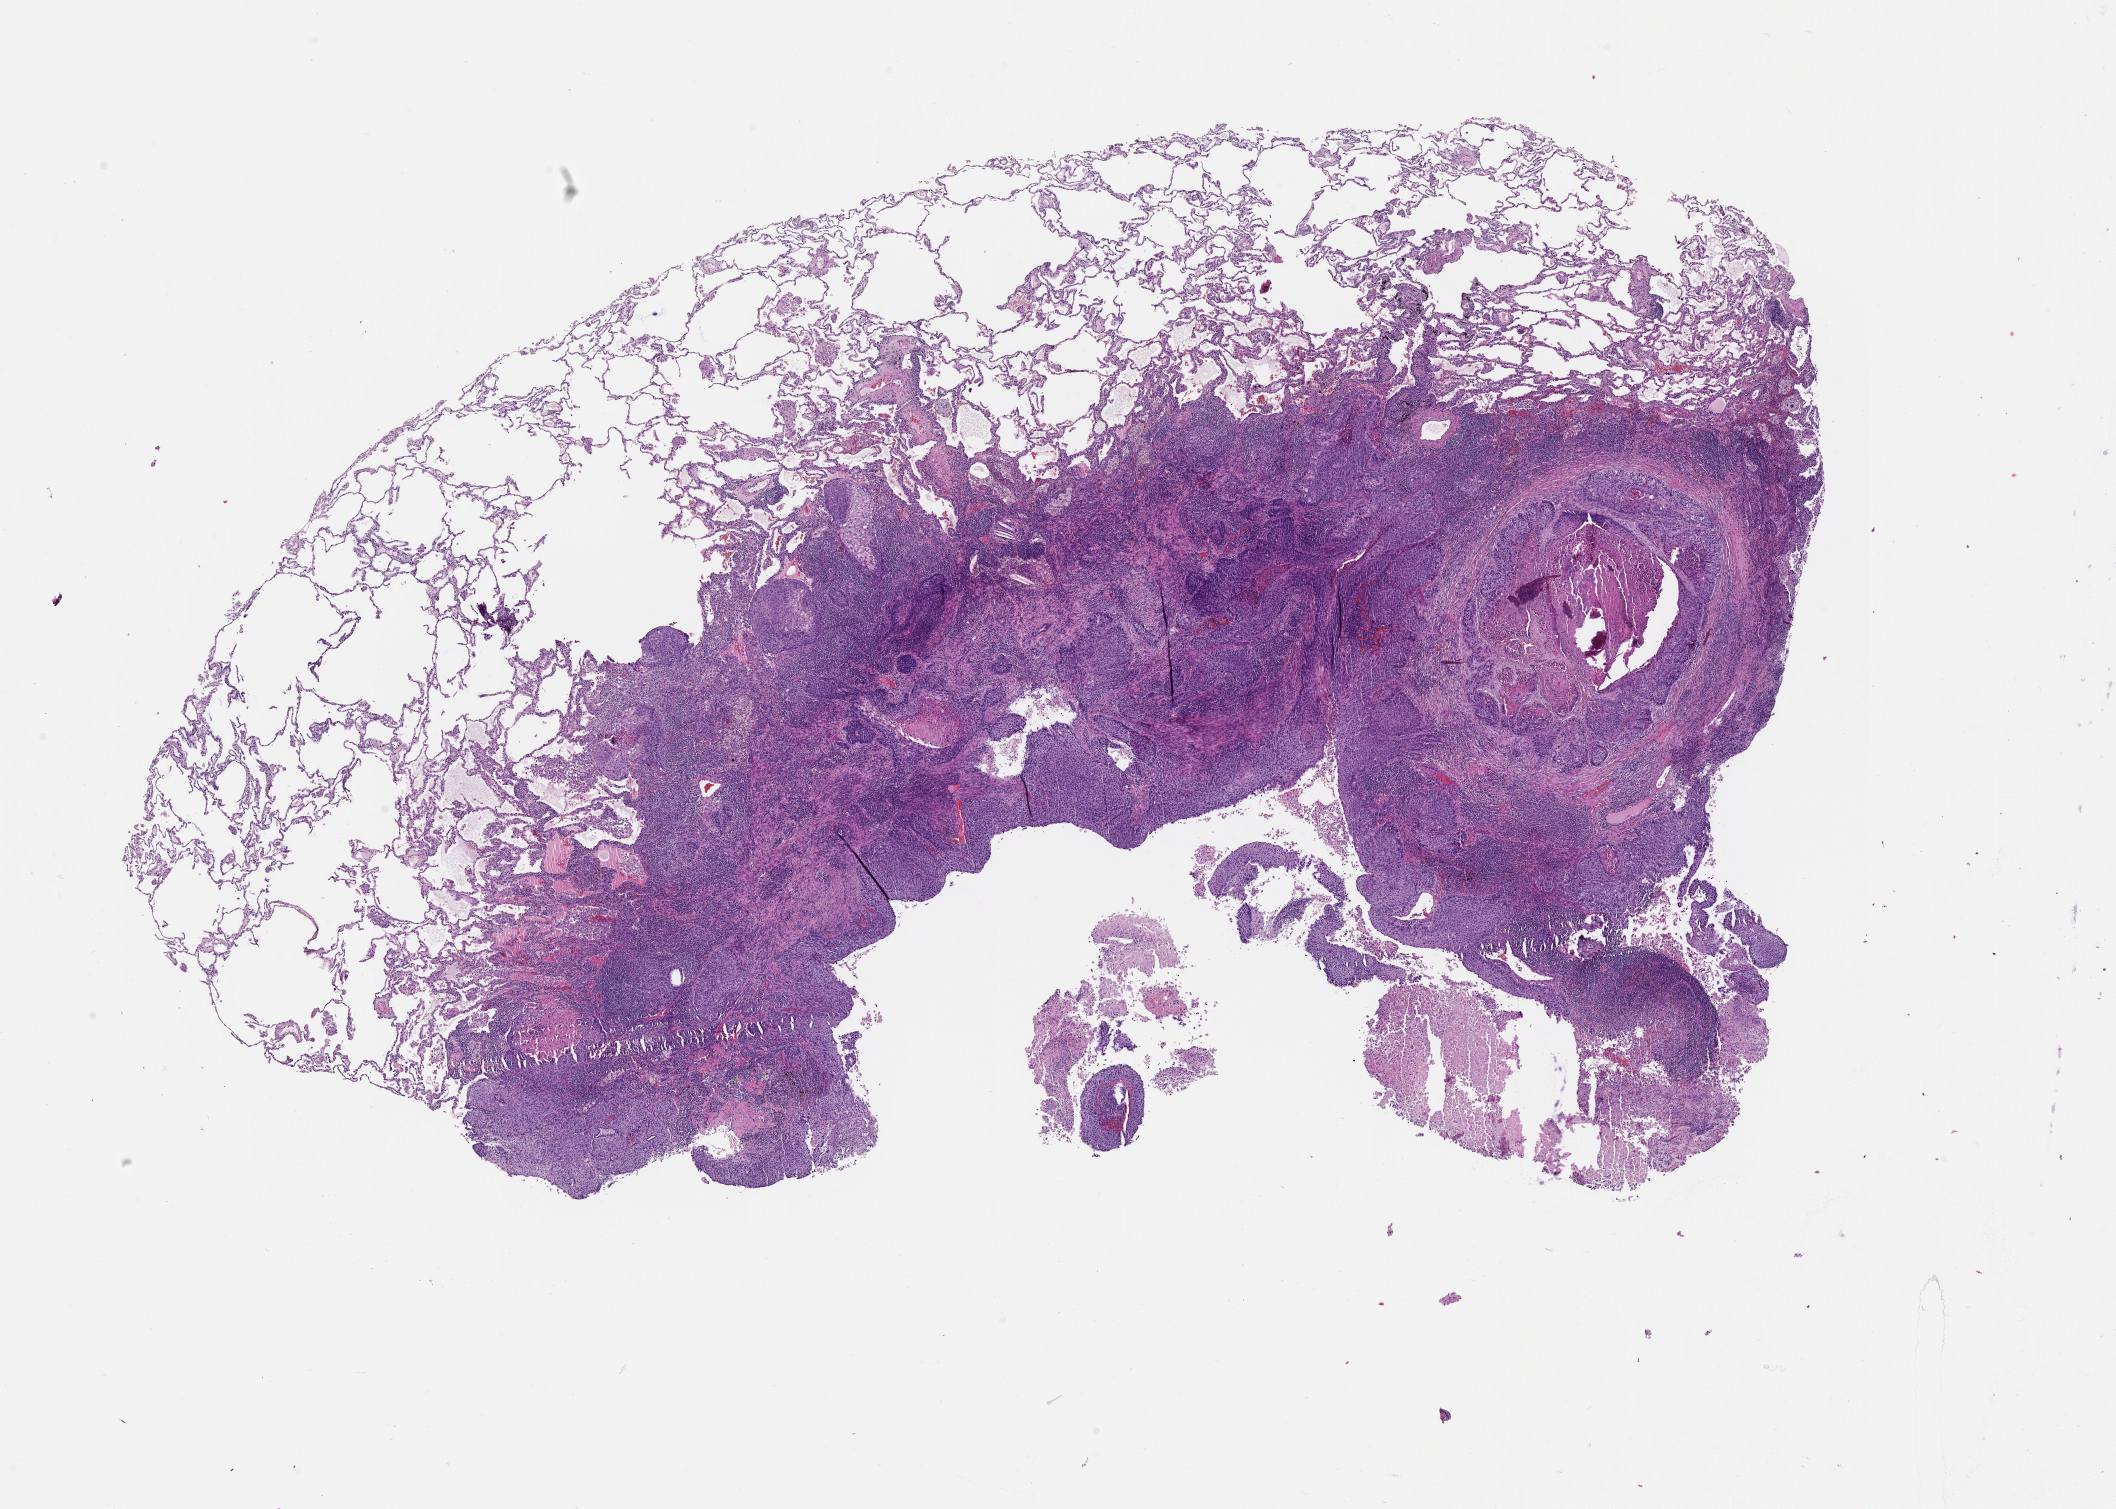
H&E whole-slide image, a low-resolution overview of the entire scanned area, about 17.0 x 12.1 mm (slide scanned at 20x); lung, tumour tissue. 67-year-old male patient.
Patient diagnosis (cohort enrolment): squamous cell carcinoma (lung).